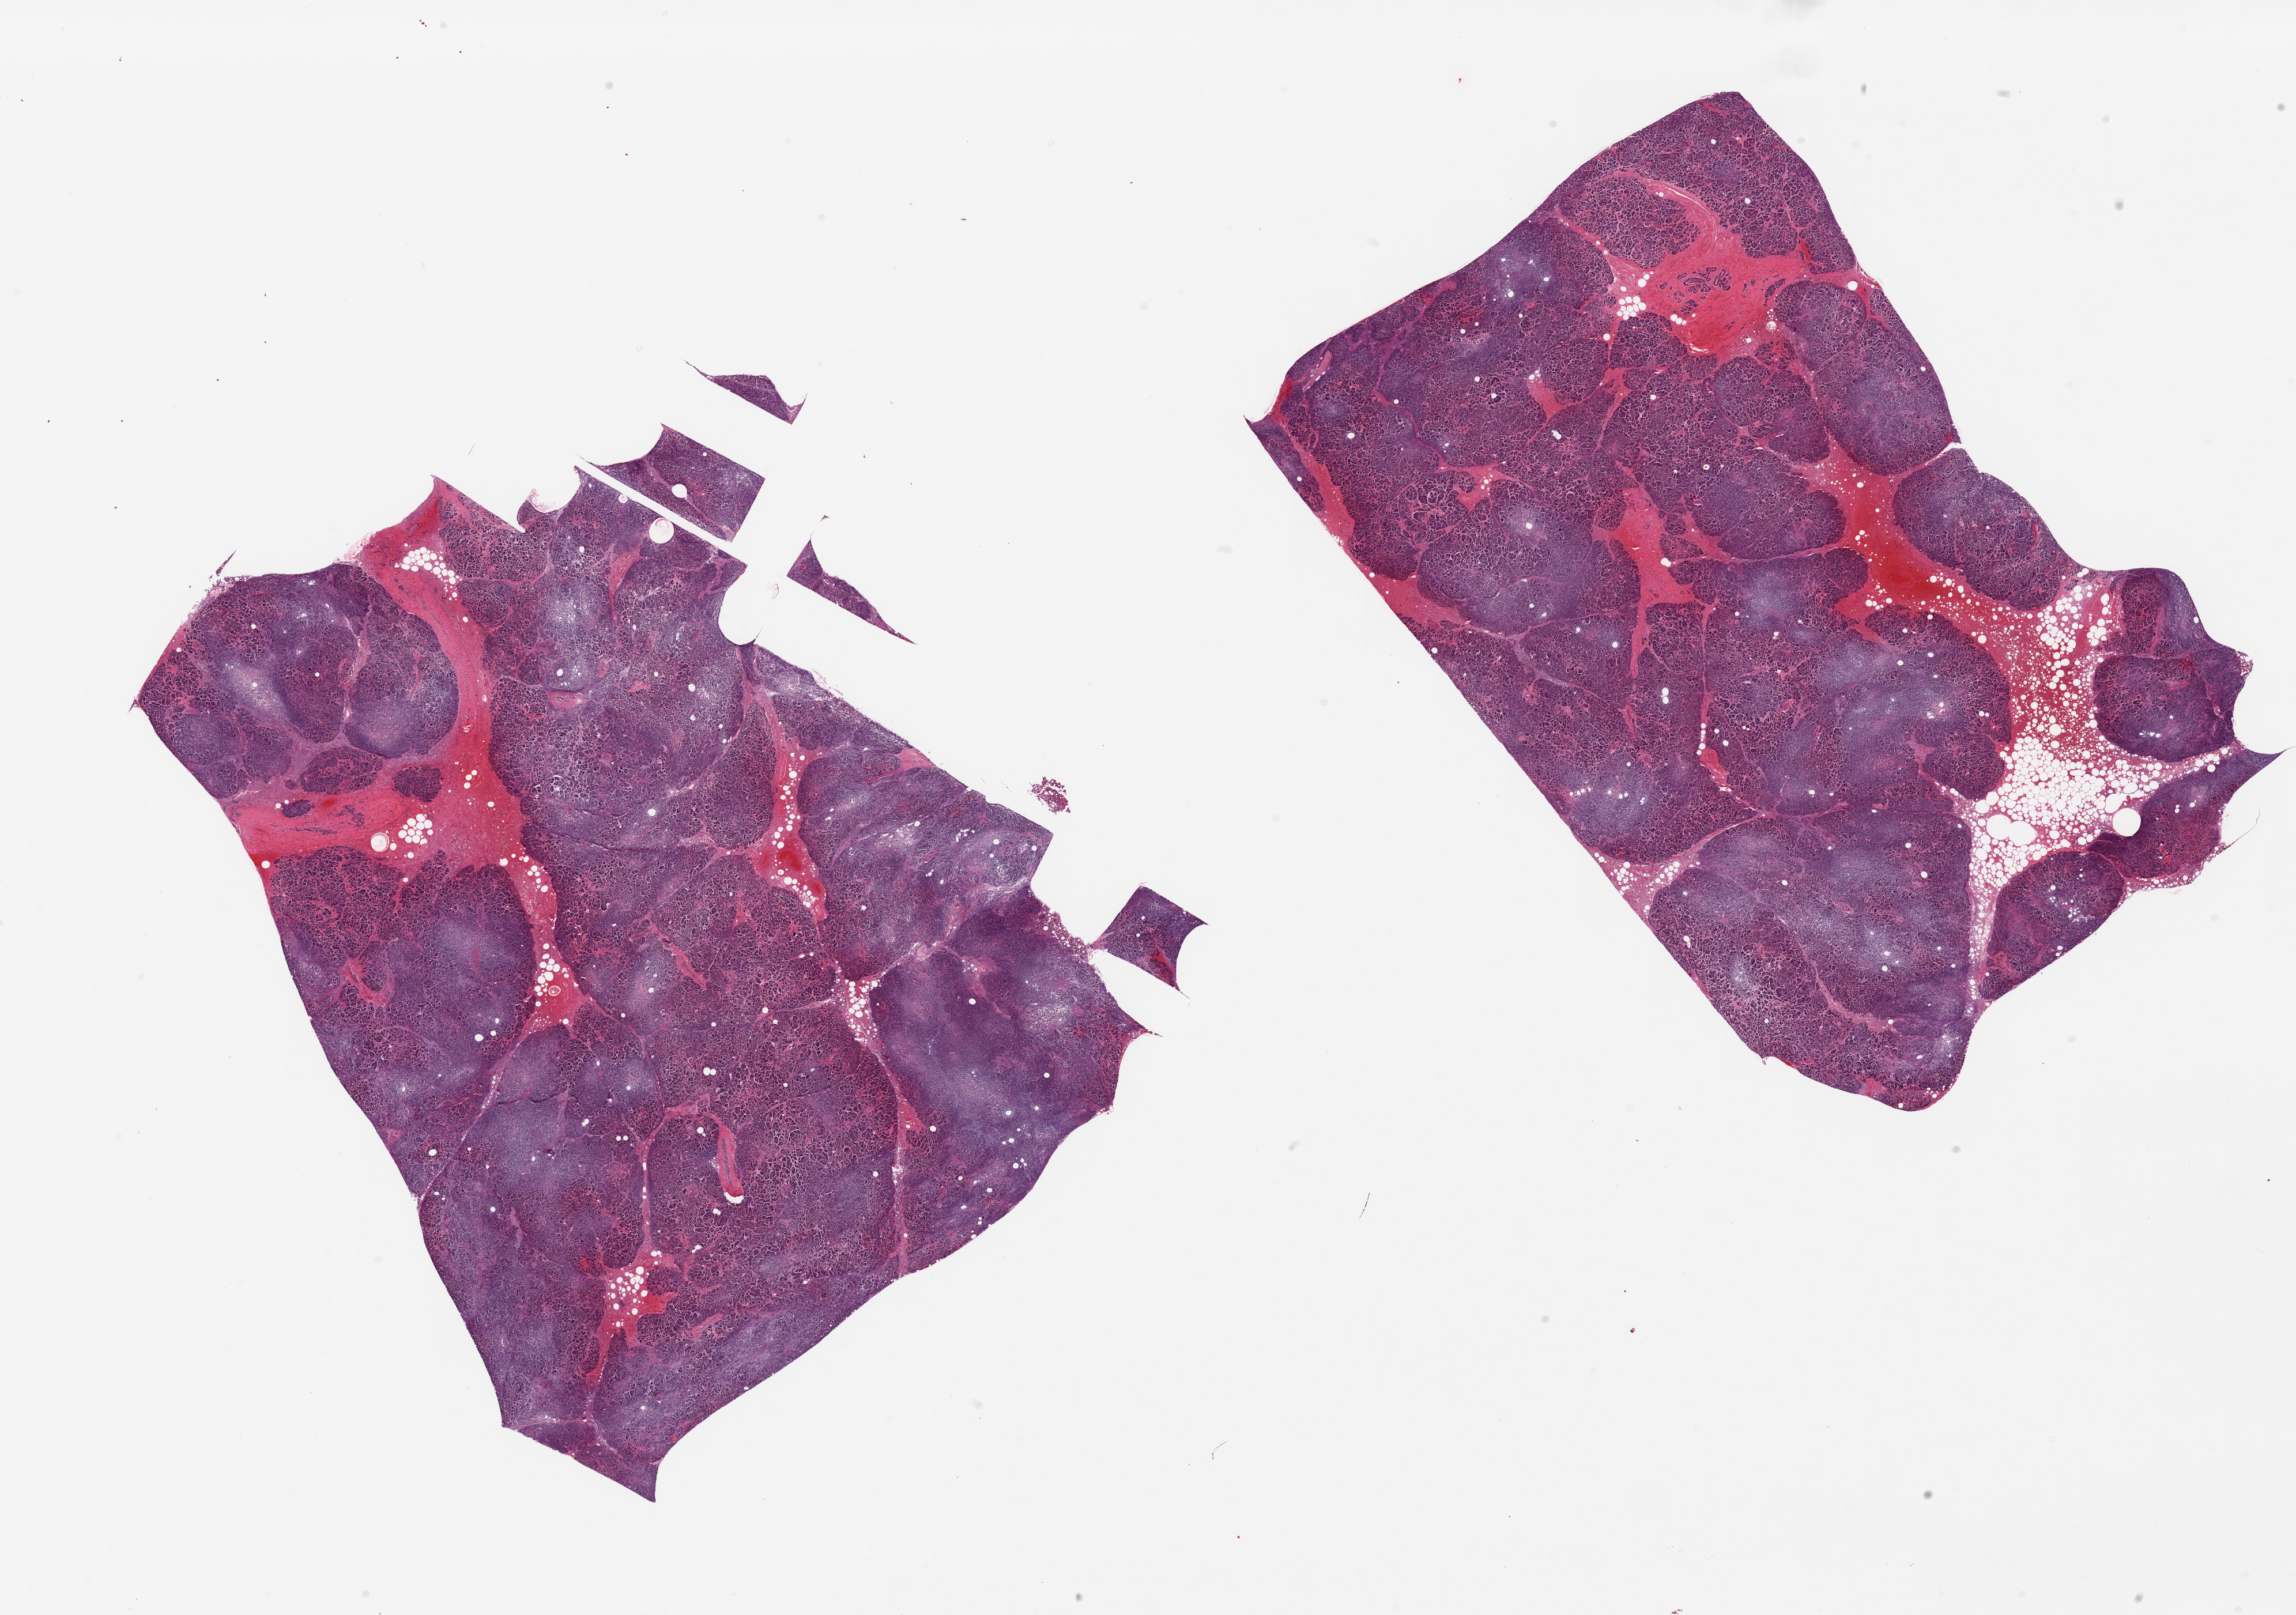
Haematoxylin and eosin whole-slide image — whole scanned area (about 31.5 x 22.2 mm, from a 20x scan) shown as a low-resolution overview, PAXgene-fixed paraffin-embedded (PFPE) section, target tissue: pancreas, donor tissue sample. Male donor.
Review note (as recorded): 2 pieces, marked autolysis/saponification, approaching score 3. Islets not well visualized.